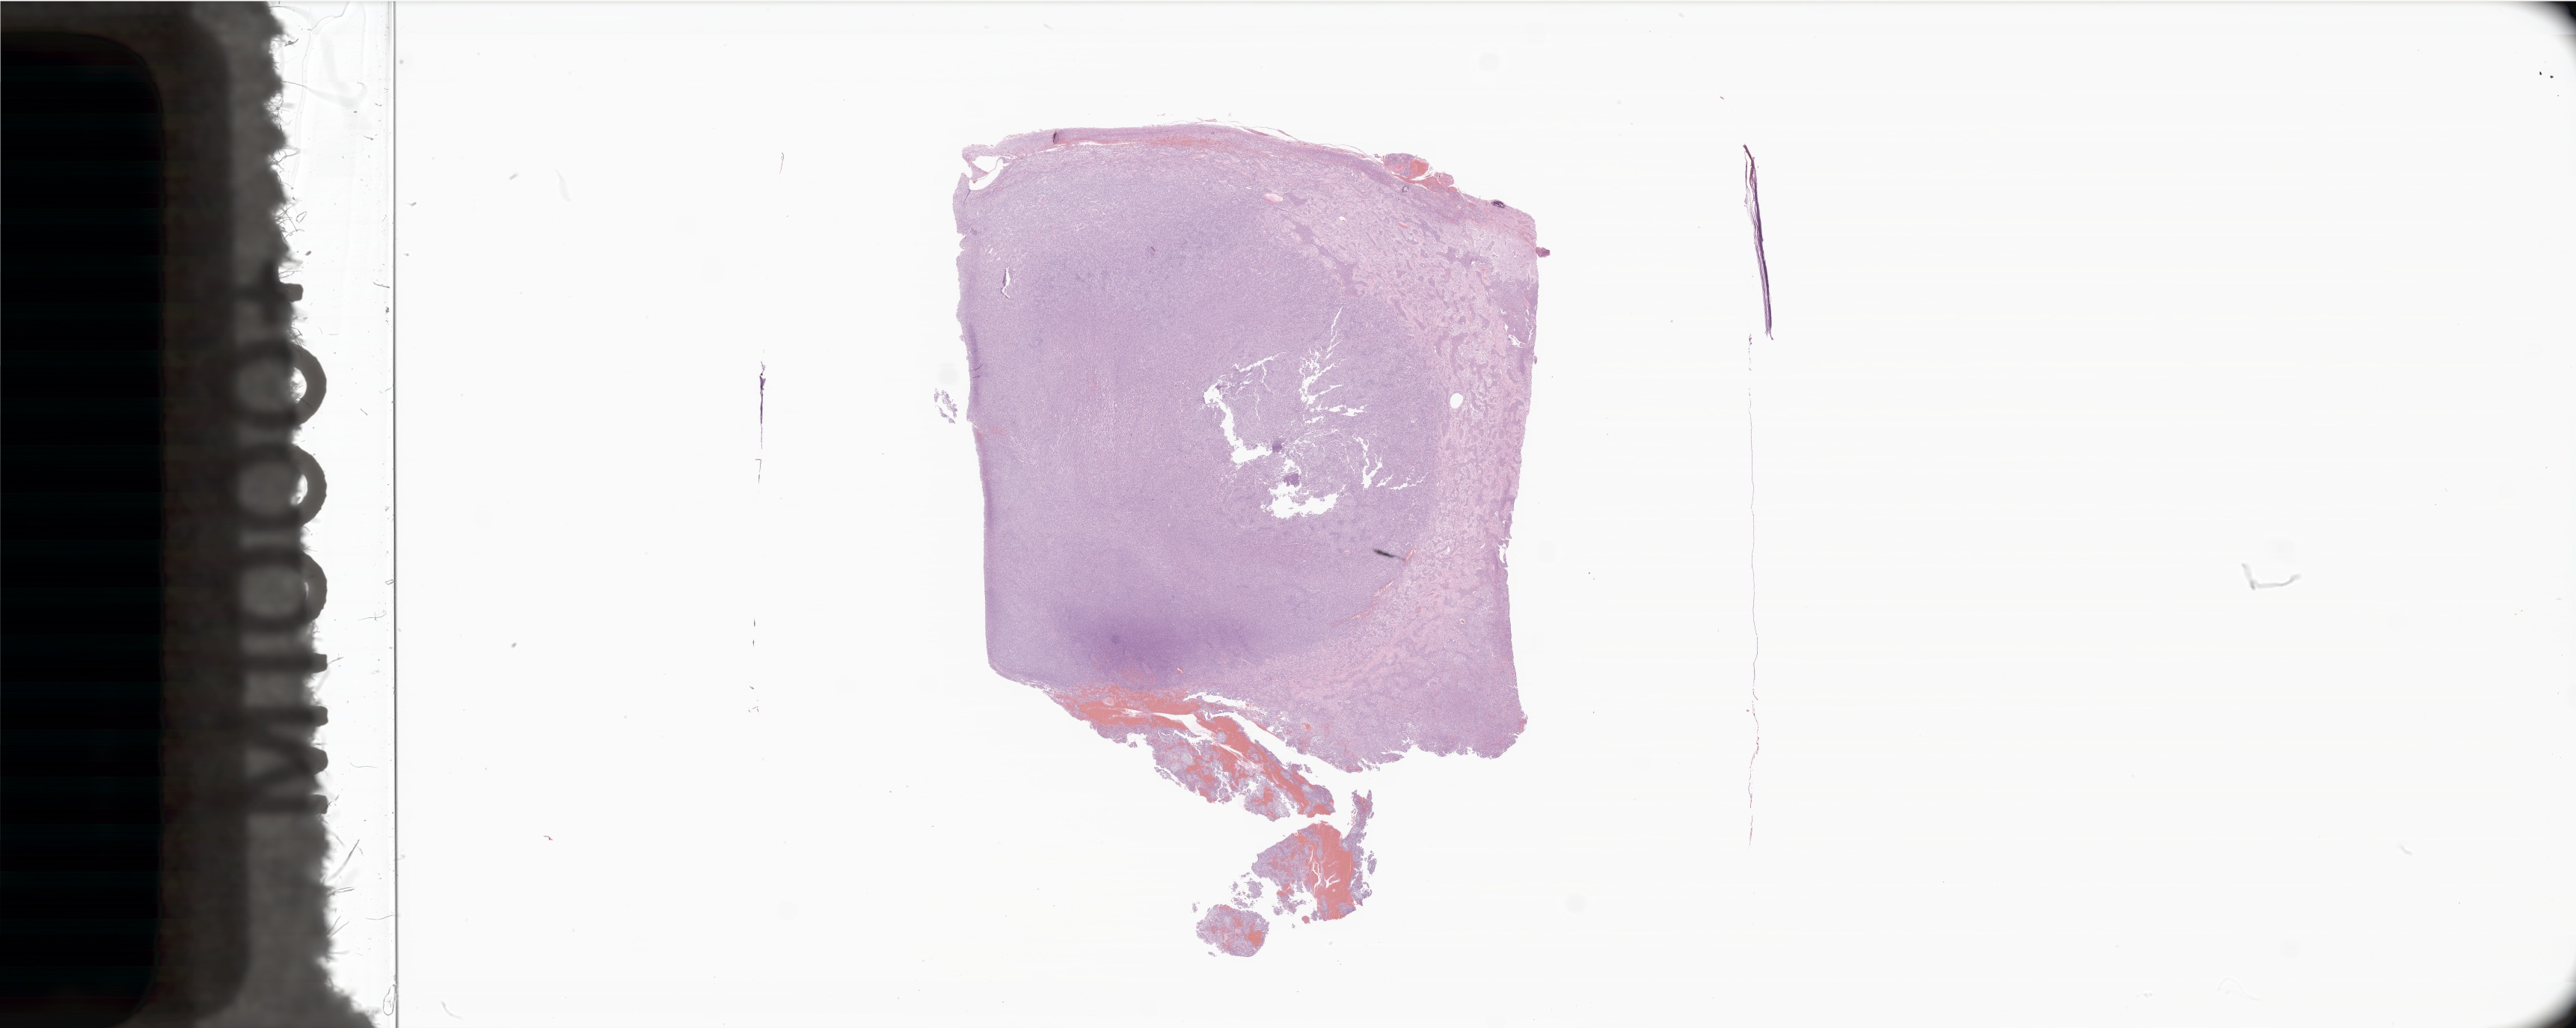
Digitized H&E-stained section of tumor tissue from the brain — shown as a low-resolution overview of the whole scanned area (about 58.1 x 23.2 mm), formalin-fixed, paraffin-embedded (FFPE) tissue. Patient: female, age 305 days.
- diagnosis (ICD-O-3 morphology term): Neoplasm, uncertain whether benign or malignant